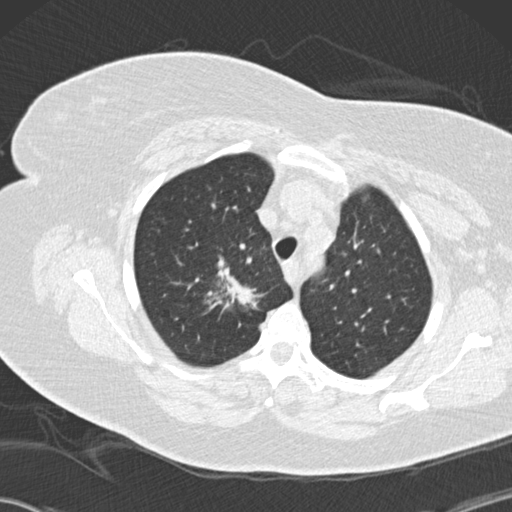
Low-dose screening chest CT, one axial slice. Slice 115 of 146 in the series (ordered by position). Lung window (W 1500 / L -600 HU). 2 mm slice thickness. 512 × 512 image matrix, field of view 350 × 350 mm.
Structures marked on this image (expert manual segmentation):
- lesion 1 (tumor, upper lobe of right lung): bounding box (x1, y1, x2, y2) in pixels: (207, 257, 262, 310)